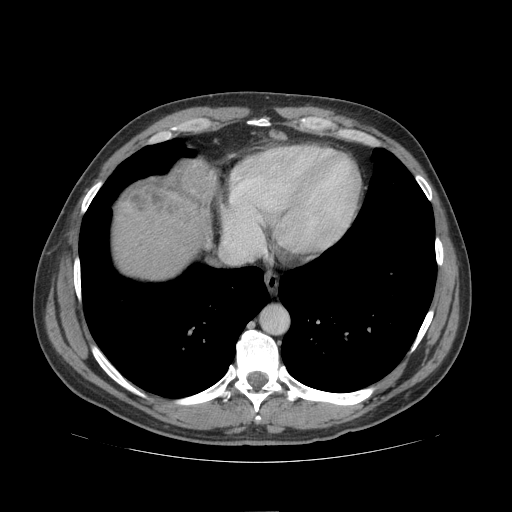
Contrast-enhanced abdominal CT (liver protocol), one axial slice. Slice 95 of 109 in the series (ordered by position). Soft-tissue window (W 400 / L 40 HU). 2.5 mm slice thickness. 512 × 512 image matrix, field of view 420 × 420 mm. Case-level facts recorded for this patient, not image findings: diagnosis: hepatocellular carcinoma (patient treated with transarterial chemoembolisation; whether this scan precedes or follows treatment is not stated here); TNM stage (as recorded): Stage-IIIB; Child-Pugh class: A; tumour nodularity: multinodular.
Outlined on this slice (semi-automatically segmented with operator editing):
- liver parenchyma outside the tumour (the mass and vessels are separate outlines, so this box may not span the whole liver): box from (x=114, y=160) to (x=216, y=280) px
- mass: (x=125, y=161)–(x=215, y=222)